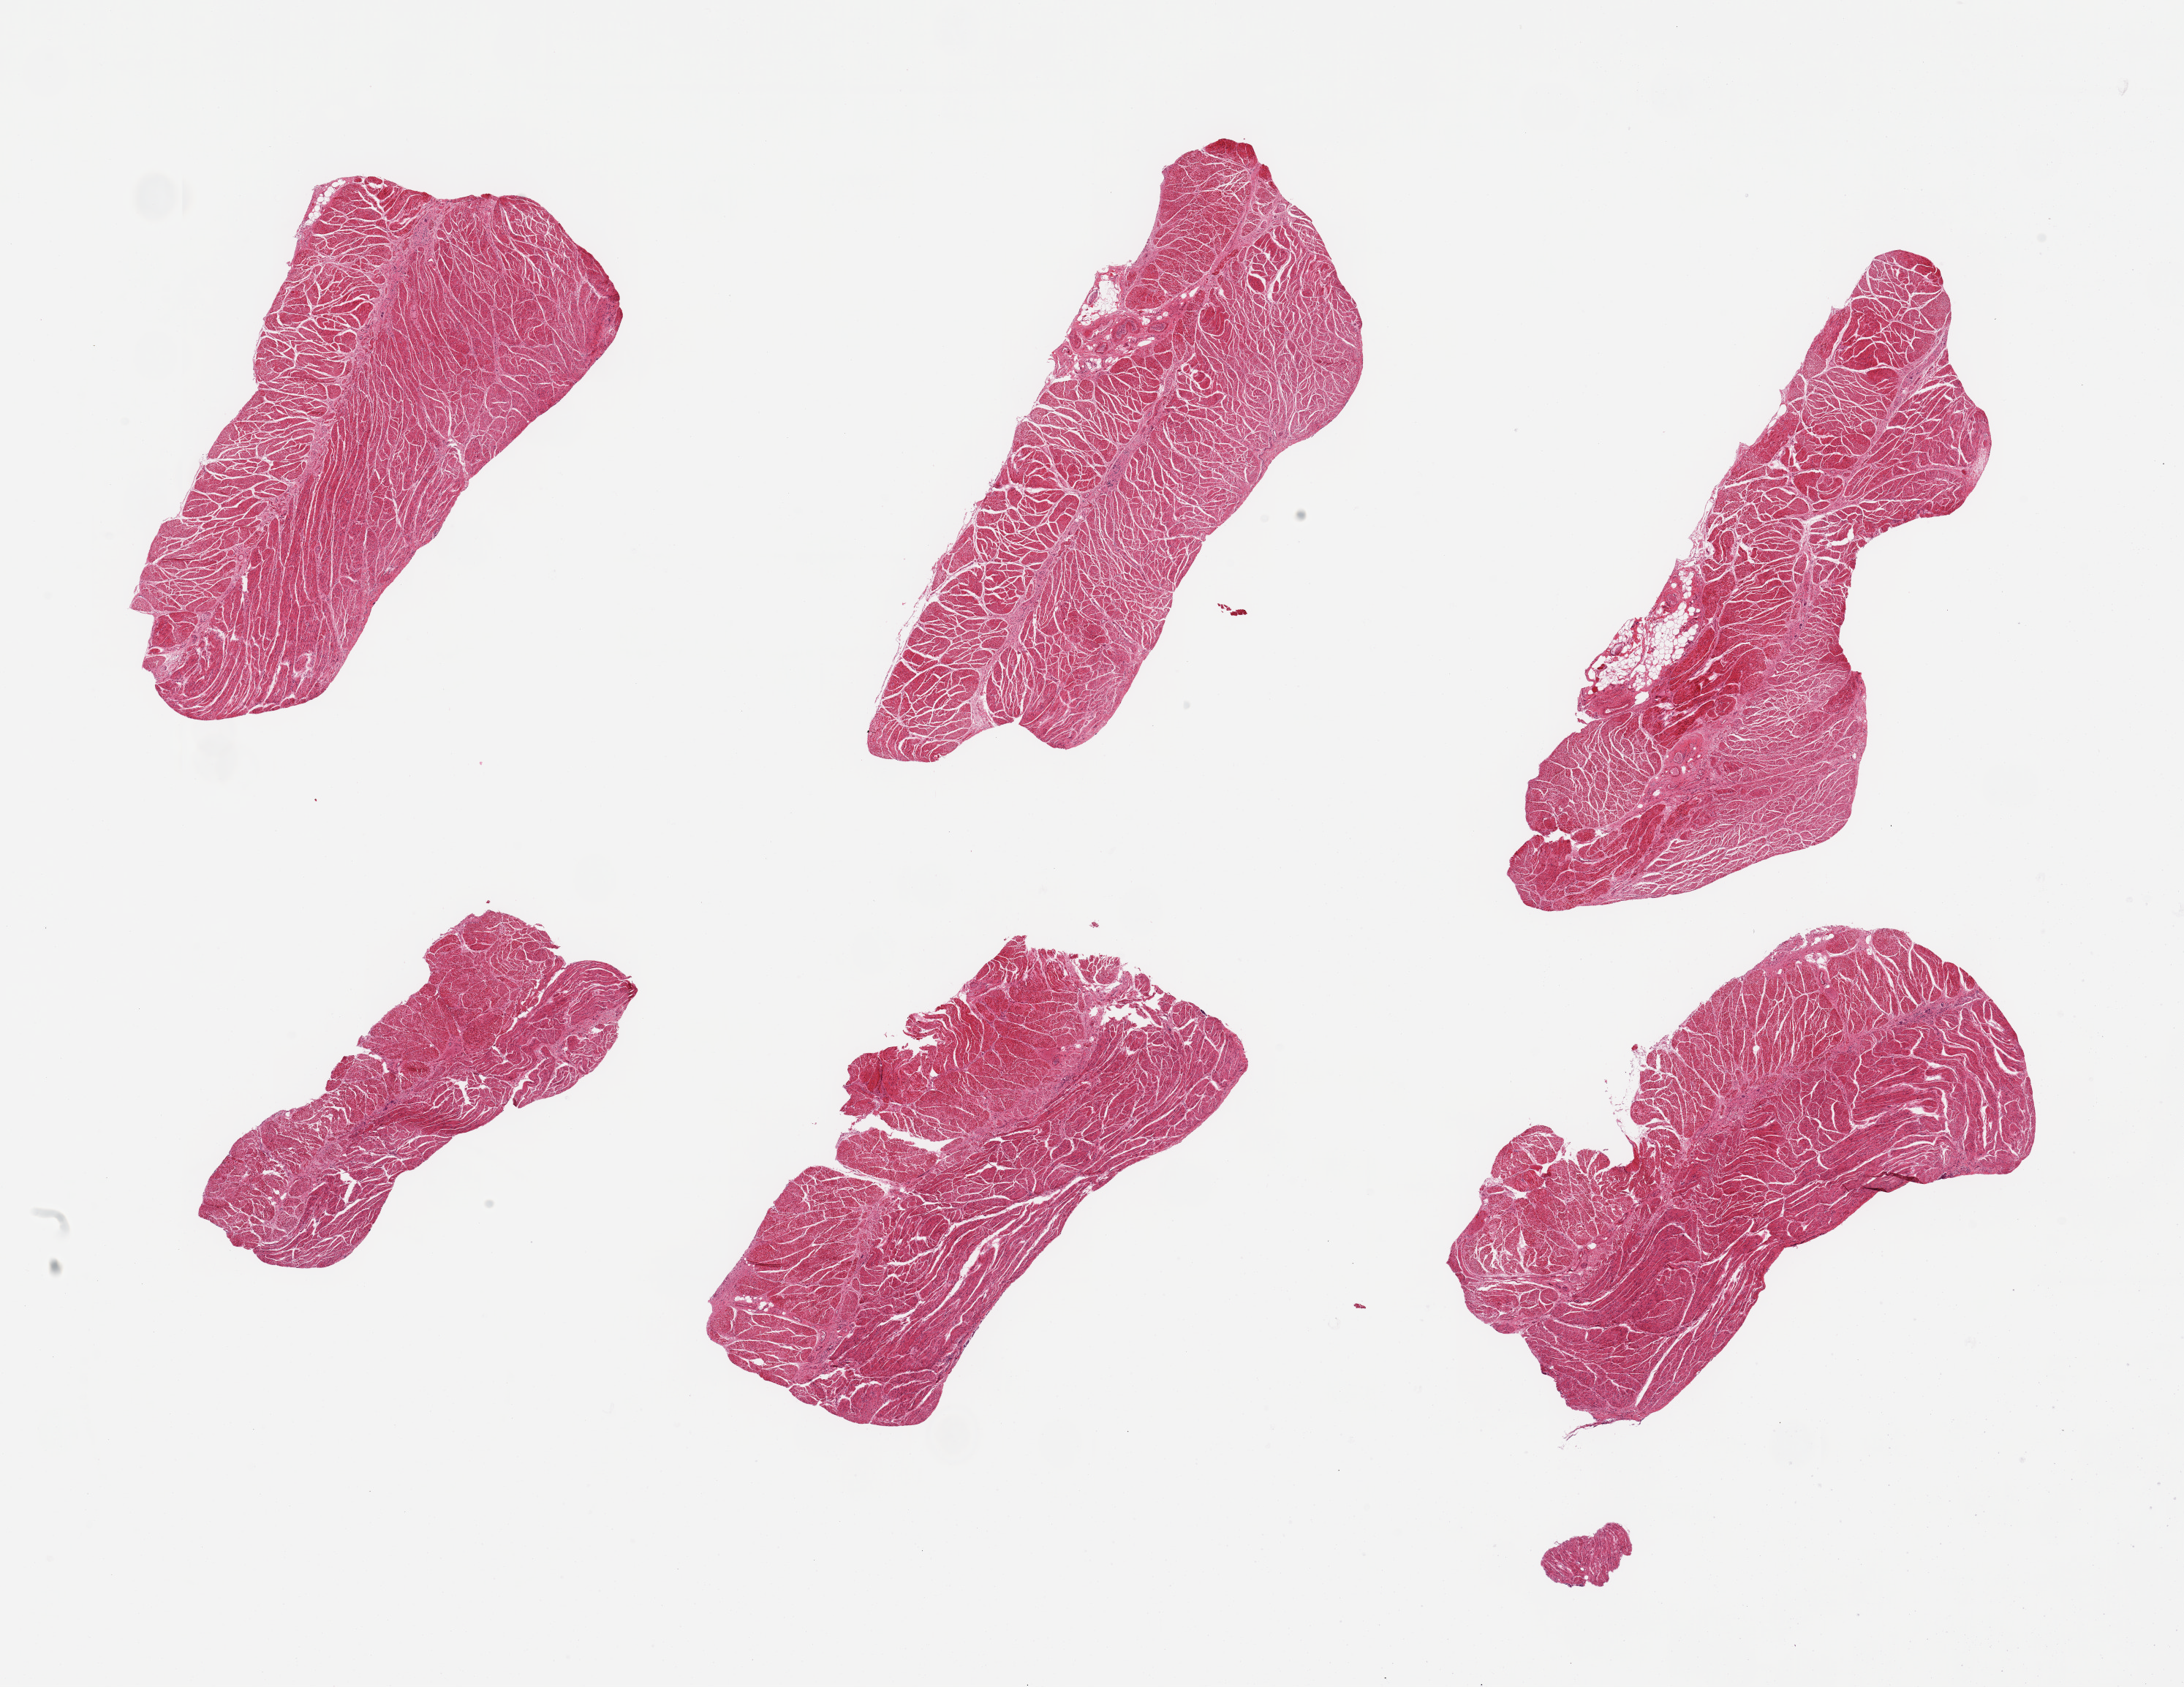
Whole-slide image, H&E stain — shown as a low-resolution overview of the whole scanned area (about 23.6 x 18.2 mm, acquisition: 20x scan), PAXgene-fixed, paraffin-embedded tissue, target tissue: esophageal muscle, tissue donor sample. Donor: male.
Reviewer comment on this tissue sample: 6 pieces; well trimmed muscle.